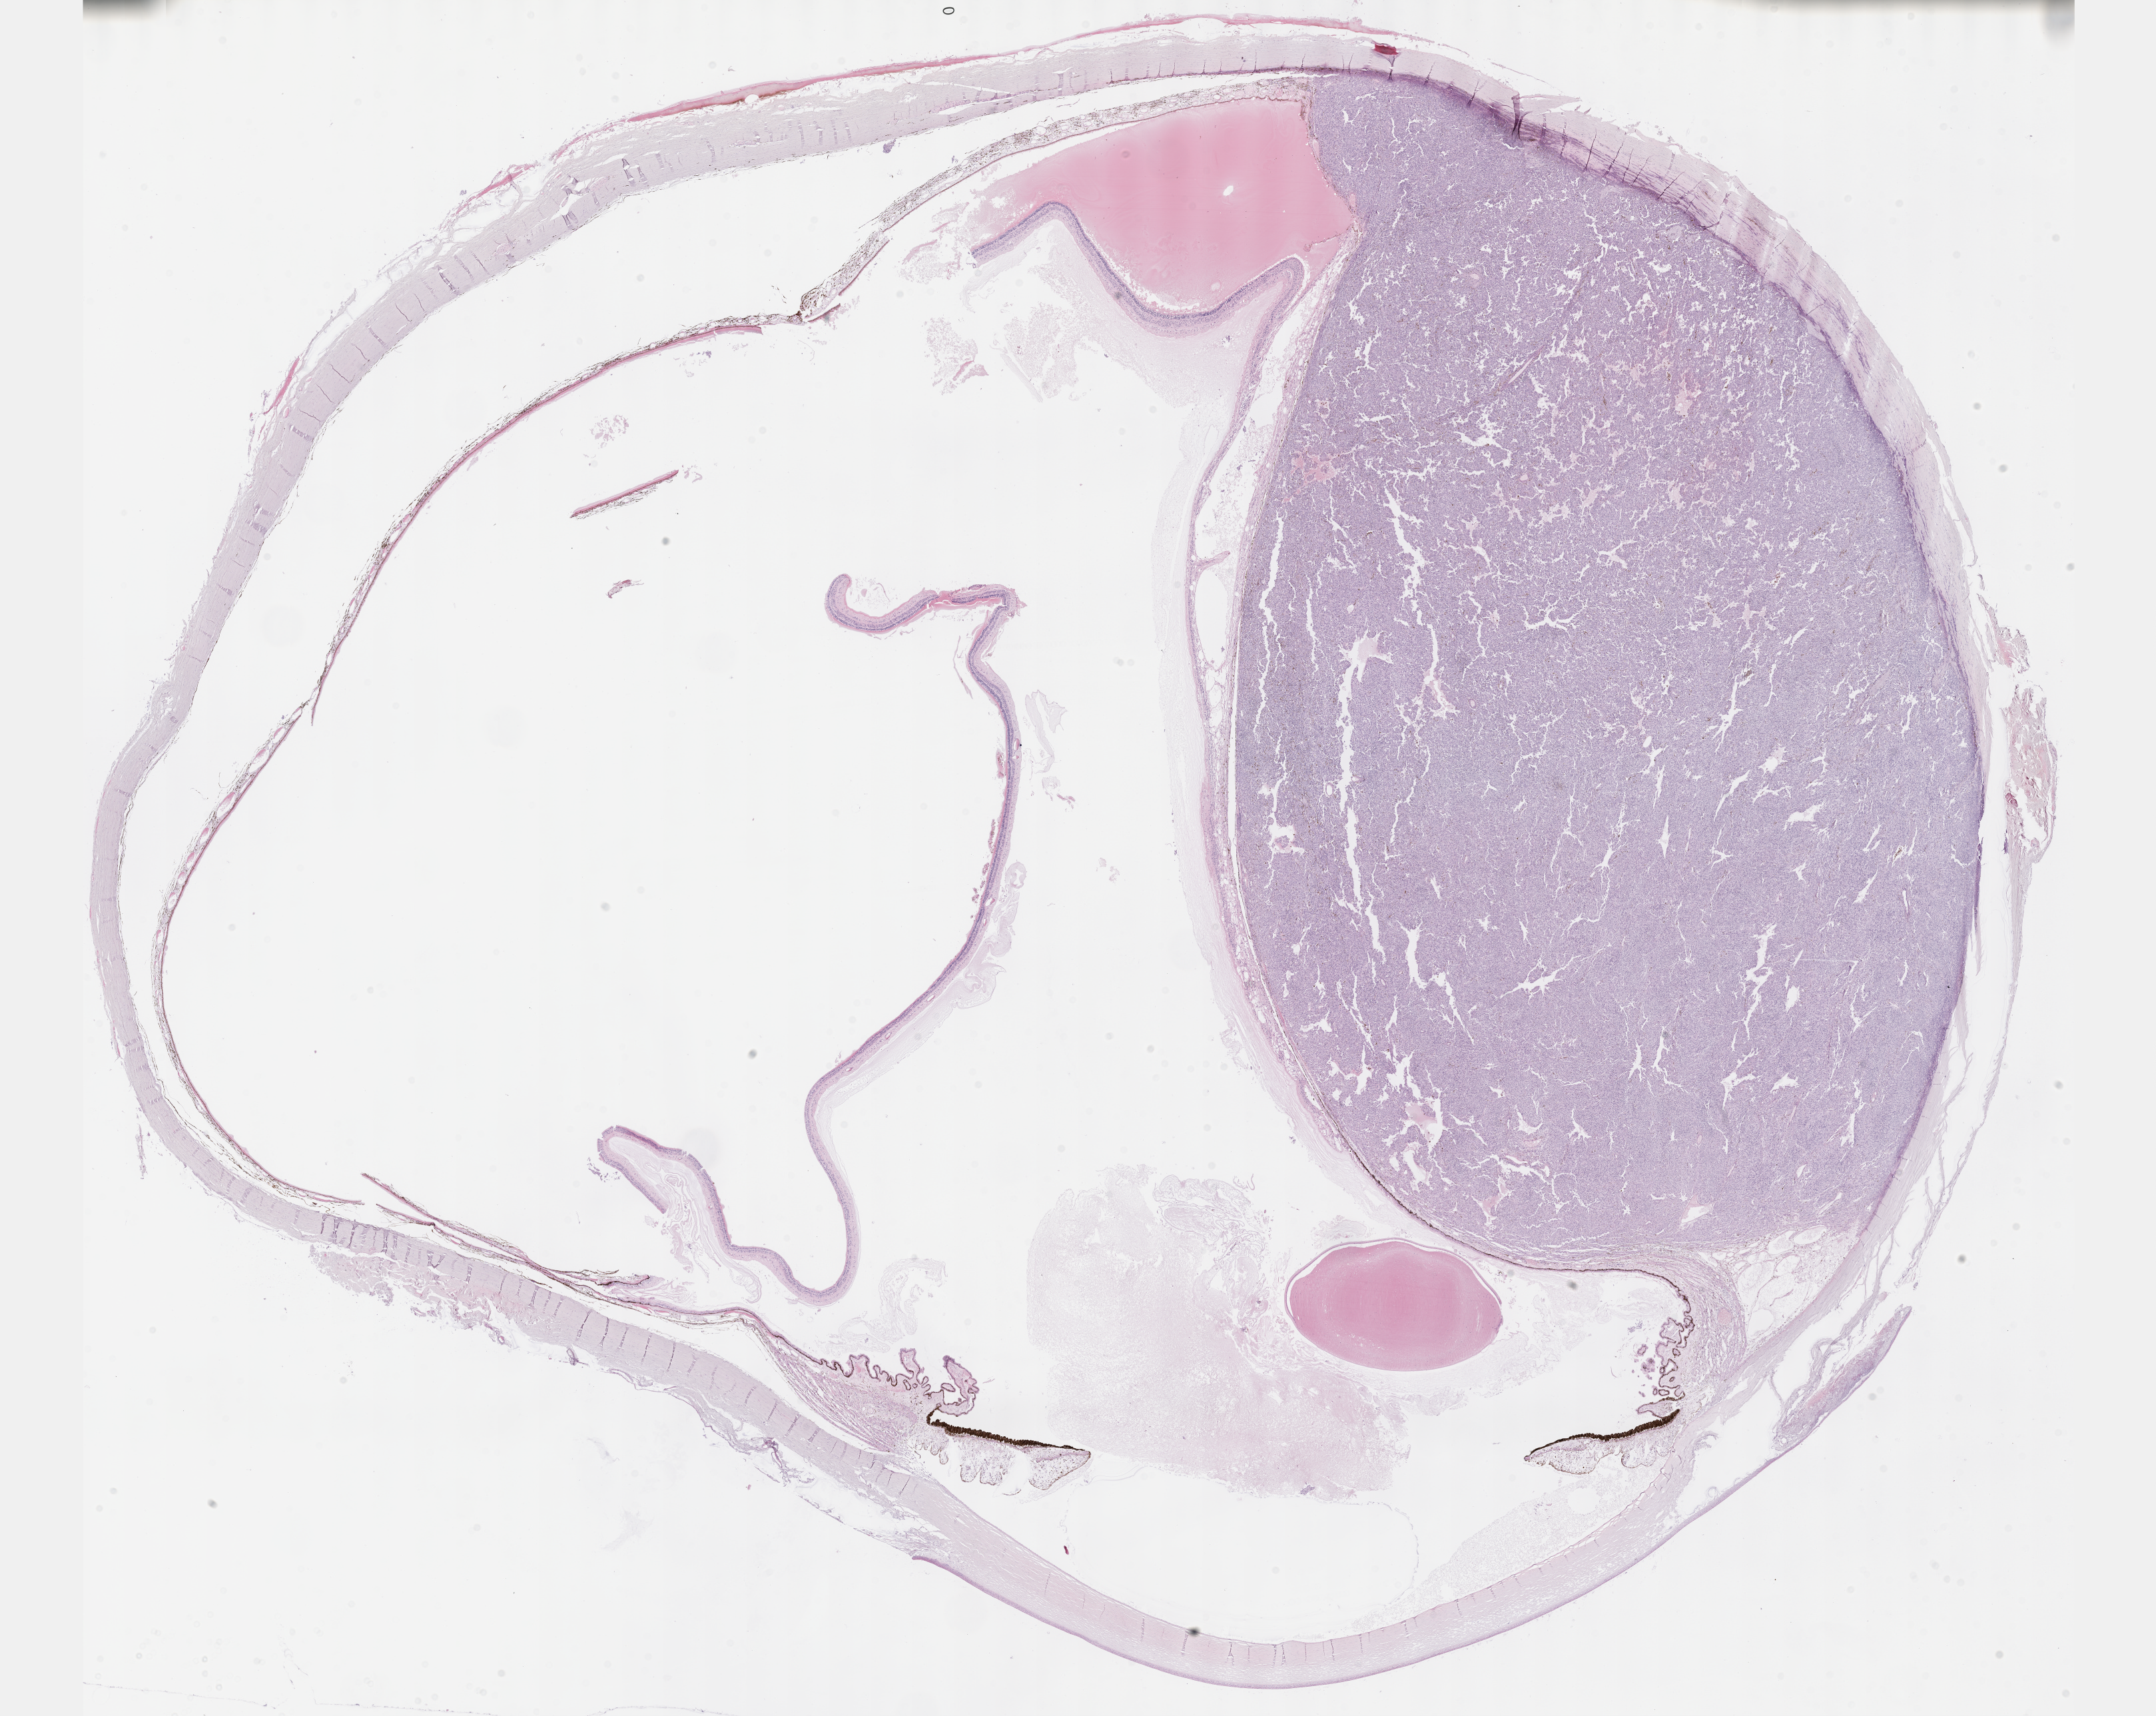
Digitized H&E-stained tissue section (whole slide) — shown as a low-resolution overview of the whole scanned area (about 26.2 x 20.8 mm), formalin-fixed paraffin-embedded (FFPE) diagnostic section, uvea, primary tumour sample. Patient: male, age at initial diagnosis 53 years.
Histologic diagnosis: Epithelioid cell melanoma (choroid).